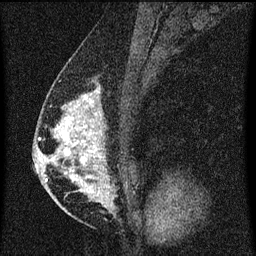
Breast MRI (dynamic contrast-enhanced), one sagittal slice; slice 33 of 60 in the series (ordered by position); dynamic contrast-enhanced series, image 2 of 3 at this slice position (ordered by acquisition); 1.5 T; TE 4.2 ms, TR 8 ms; 256 × 256 image matrix, field of view 180 × 180 mm. Female patient, age 47 years.
Annotated regions visible in this slice (semi-automatically segmented with operator editing):
- analysis volume of interest (the breast-tissue region the enhancement analysis was run in; not a lesion): bounding box <50,80,135,203> (left, top, right, bottom; pixels)
- tumour enhancement mask (voxels above the 70 % enhancement threshold inside the analysis volume of interest): <50,92,105,195>